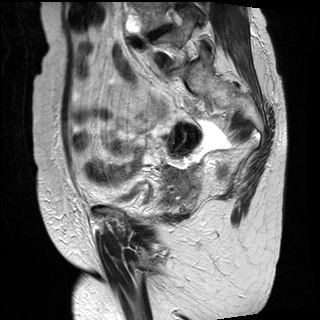
Pelvic MRI for cervical cancer, one sagittal slice. Position 9 of 30 along the scan axis. T2-weighted. 1.5 T. TE 89 ms, TR 2930 ms. 320 × 320 image matrix, field of view 260 × 260 mm. Patient: female, 61 years.
Outlined on this slice (manually delineated by an expert):
- uterus and cervix: bounding box [x1, y1, x2, y2] px = [157, 161, 204, 208]